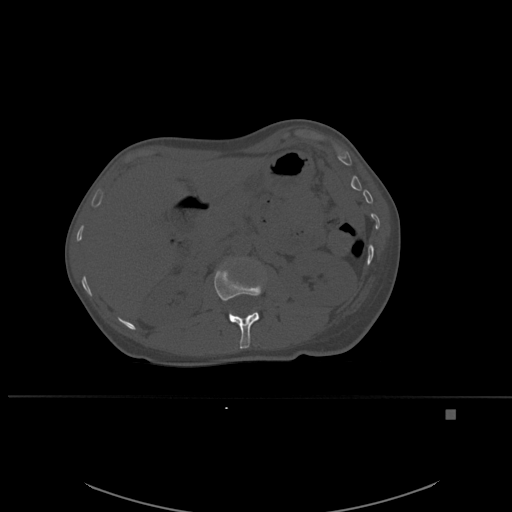
CT including the spine, one axial slice; slice 253 of 537 in the series (ordered by position); bone window (W 1800 / L 400 HU); 512 × 512 image matrix, field of view 440 × 440 mm. Female patient, age 45 years. From the clinical record (not read from this slice): primary cancer: lung.
Structures marked on this image (semi-automatic segmentation, software-assisted and operator-edited):
- L1 vertebra: bounding box (x1, y1, x2, y2) in pixels: (214, 262, 263, 349)
- L2 vertebra: (242, 258, 248, 261)